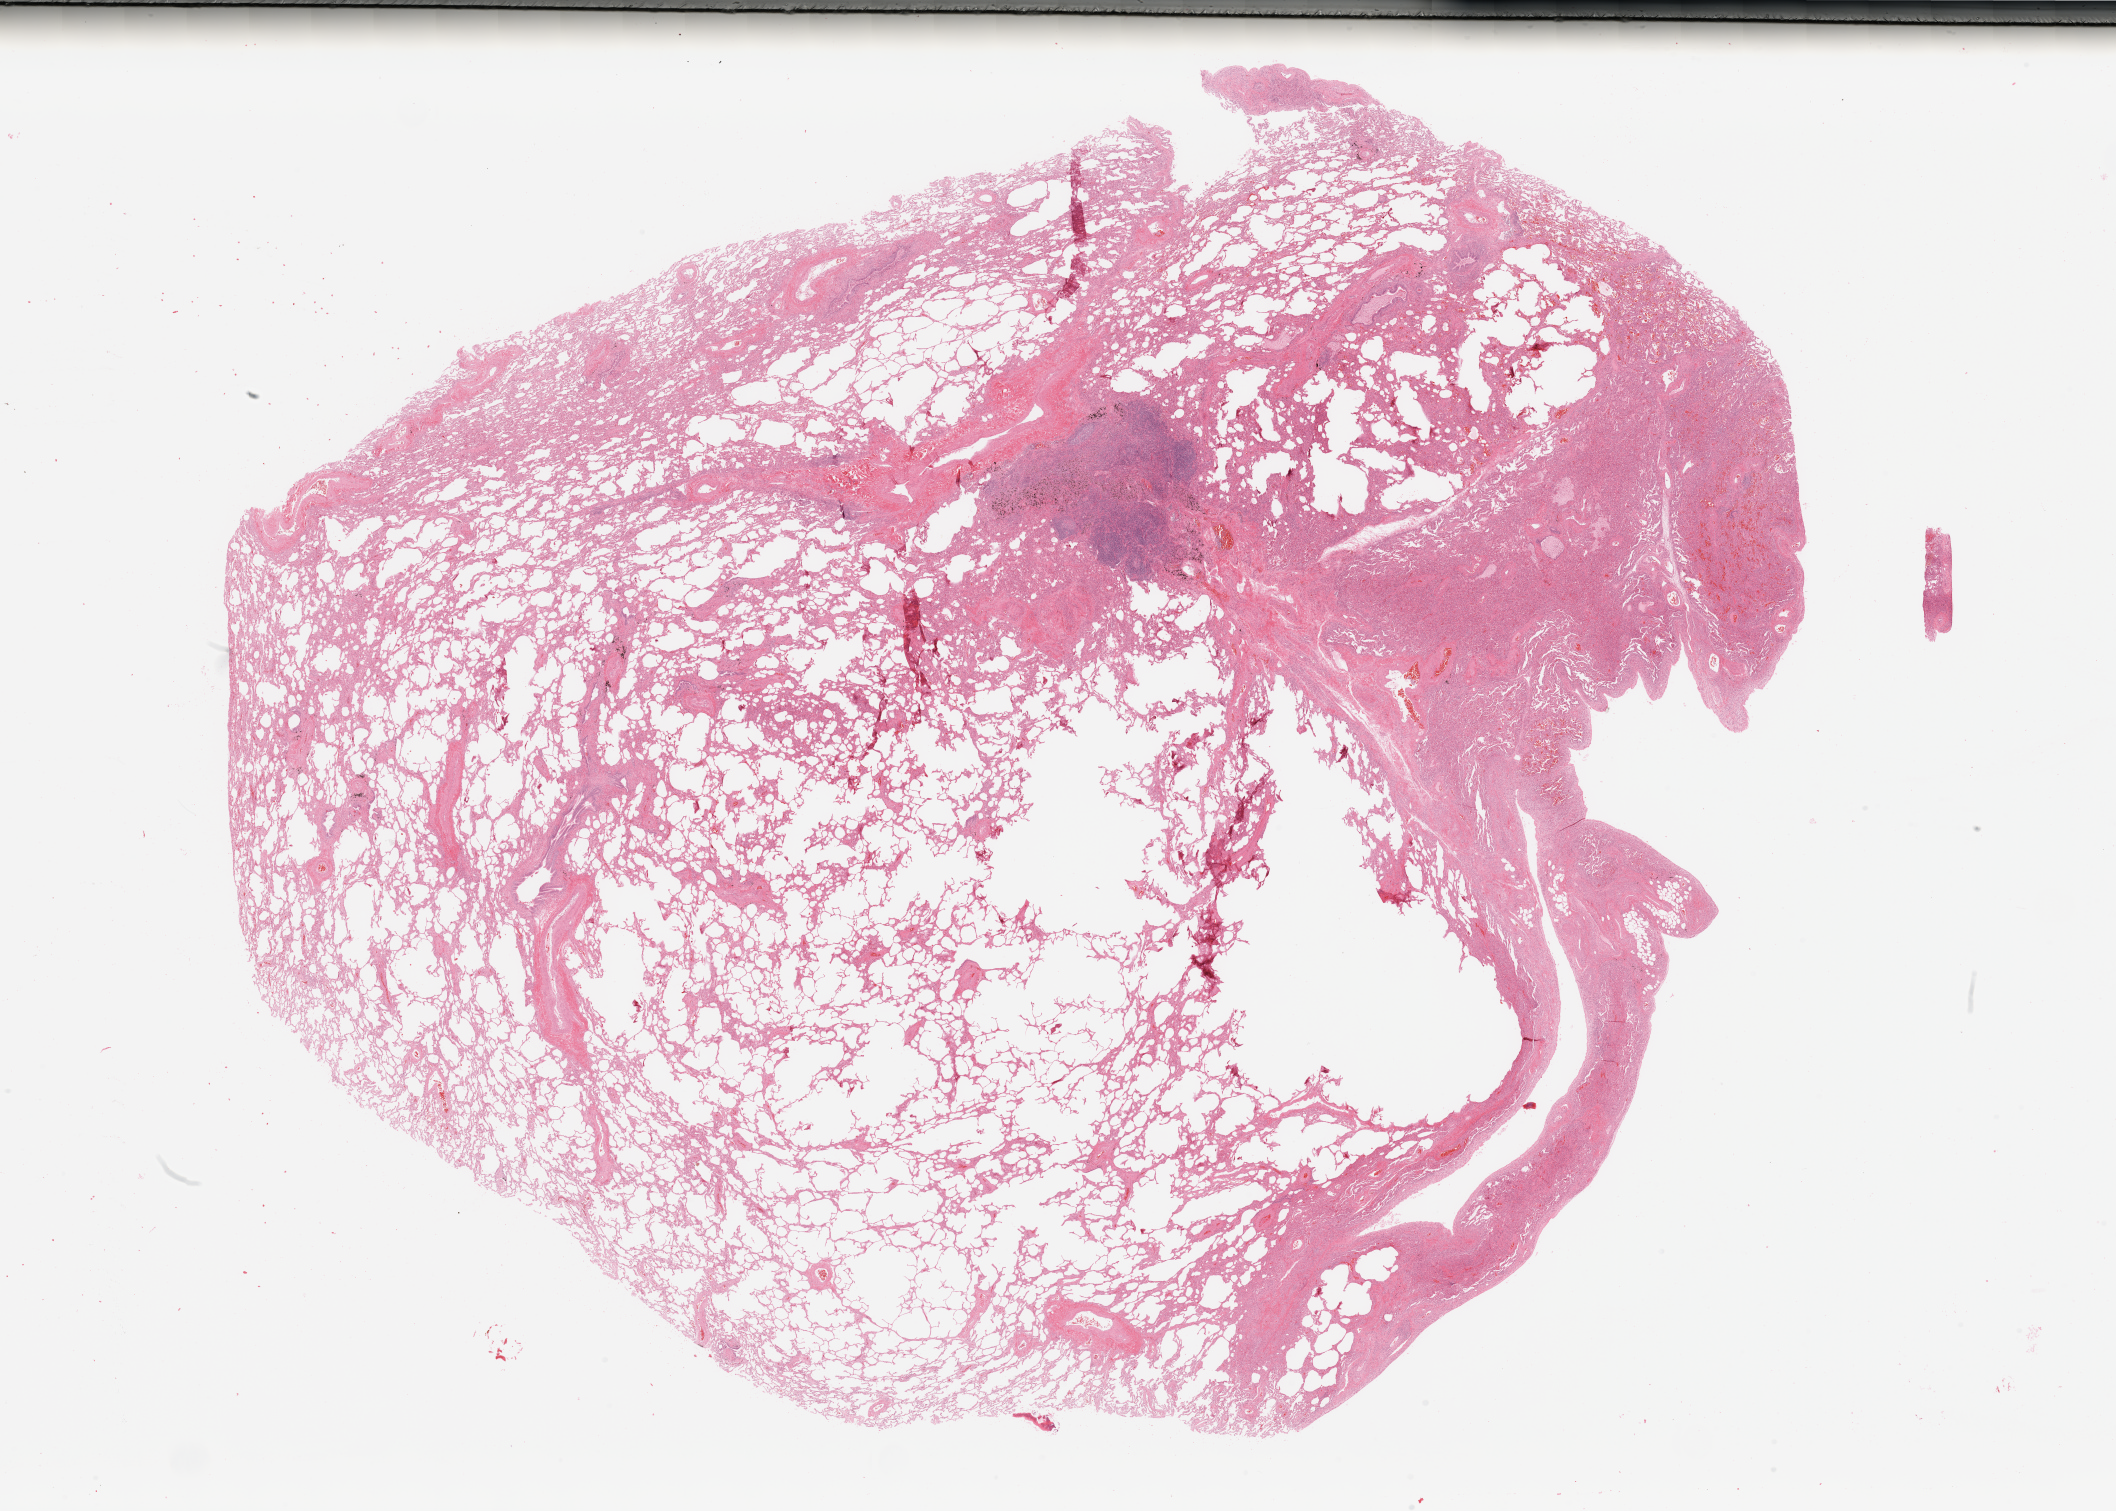
Hematoxylin and eosin (H&E) stained whole-slide image, a low-resolution overview of the entire scanned area, about 33.5 x 23.9 mm; lung, normal (non-tumour) tissue. 48-year-old female patient.
This section: normal (non-tumour) tissue from the same patient. Patient diagnosis: Adenocarcinoma, NOS.